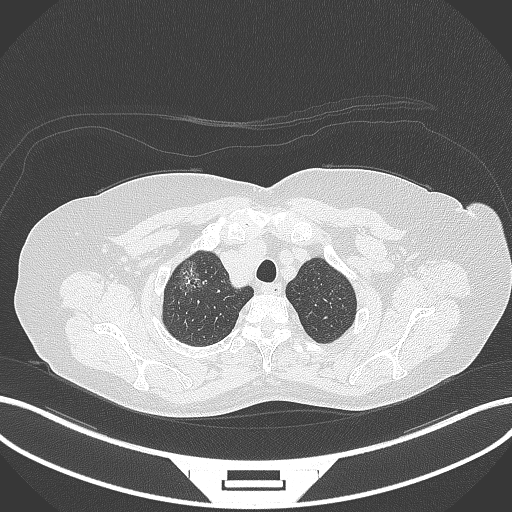
Chest CT, one axial slice; position 308 of 365 along the scan axis; reconstruction kernel B70f; 120 kVp; lung window (W 1500 / L -600 HU); 512 × 512 image matrix, field of view 400 × 400 mm. Patient: female, 62 years. Case-level facts recorded for this patient, not image findings: clinical TNM (as recorded): T1c N0 M0.
Annotated regions visible in this slice (rectangle marked by the reading radiologist):
- lung tumour (recorded histology: adenocarcinoma): box from (x=176, y=253) to (x=206, y=297) px